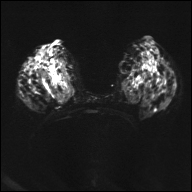
Breast MRI, one axial slice; slice 19 of 32 in the series (ordered by position); diffusion-weighted series; image 2 of 4 stored at this slice position (different b-values; order by instance number); 1.5 T; 4 mm slice thickness; 192 × 192 image matrix, field of view 360 × 360 mm. Female patient.
Structures marked on this image (expert manual segmentation):
- tumour on diffusion-weighted imaging: bounding box [x1, y1, x2, y2] px = [36, 69, 74, 103]